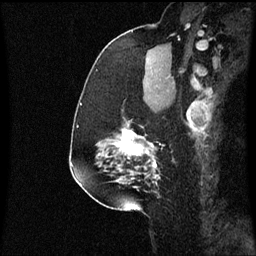
Breast MRI (dynamic contrast-enhanced), one sagittal slice; position 40 of 60 along the scan axis; dynamic contrast-enhanced series, image 2 of 3 at this slice position (ordered by acquisition); 1.5 T; TE 4.2 ms, TR 8.9 ms; 2 mm slice thickness; 256 × 256 image matrix, field of view 200 × 200 mm. Patient: female, 58 years. From the clinical record (not read from this slice): setting: breast cancer imaged before/during neoadjuvant chemotherapy; receptor status: triple-negative.
Structures marked on this image (semi-automatic segmentation, software-assisted and operator-edited):
- analysis volume of interest (the breast-tissue region the enhancement analysis was run in; not a lesion): bounding box <104,118,161,179> (left, top, right, bottom; pixels)
- tumour enhancement mask (voxels above the 70 % enhancement threshold inside the analysis volume of interest): <116,128,159,179>